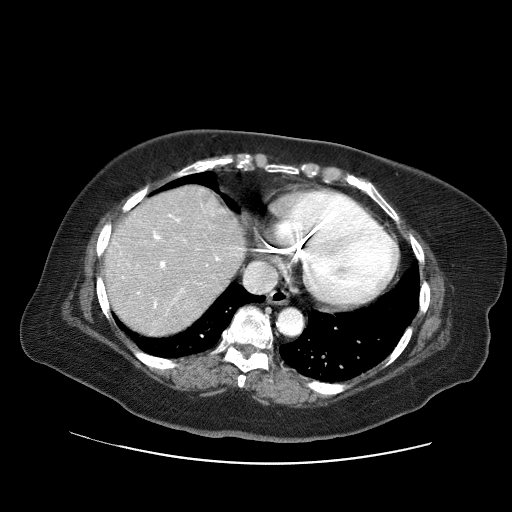
Contrast-enhanced abdominal CT (liver protocol), one axial slice. Slice 56 of 71 in the series (ordered by position). Reconstruction kernel STANDARD. 120 kVp. Soft-tissue window (W 400 / L 40 HU). 2.5 mm slice thickness. 512 × 512 image matrix, field of view 400 × 400 mm. Case-level facts recorded for this patient, not image findings: diagnosis: hepatocellular carcinoma (patient treated with transarterial chemoembolisation; whether this scan precedes or follows treatment is not stated here); TNM stage (as recorded): Stage-II; Child-Pugh class: A; tumour differentiation: poorly differentiated; tumour nodularity: multinodular.
Annotated regions visible in this slice (semi-automatic segmentation, software-assisted and operator-edited):
- liver parenchyma outside the tumour (the mass and vessels are separate outlines, so this box may not span the whole liver): bounding box (x1, y1, x2, y2) in pixels: (104, 186, 245, 334)
- liver vessels: (114, 214, 241, 308)